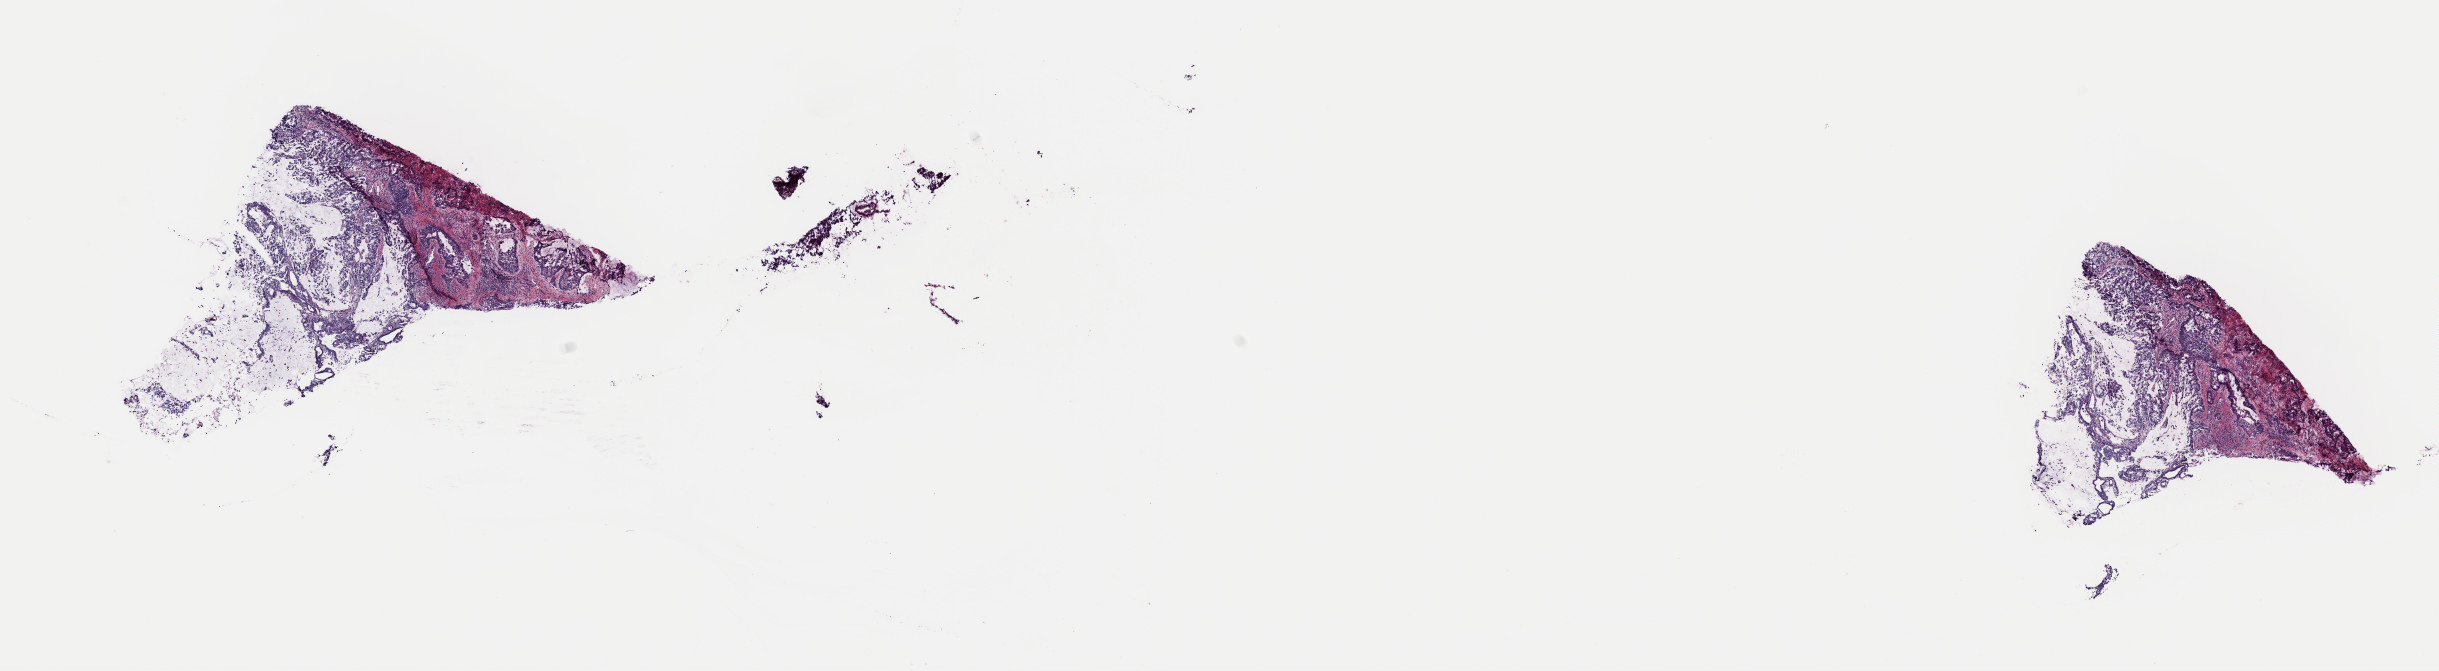
Digitized H&E-stained tissue section (whole slide) — low-resolution overview of the scanned area, about 19.3 x 5.3 mm (from a 40x scan); frozen section; stomach, primary tumour sample. Male patient; age at initial diagnosis 62 years. Slide review estimates, as recorded: tumour cells 100%, tumour nuclei 65%.
Diagnosis: Tubular adenocarcinoma (fundus of stomach).